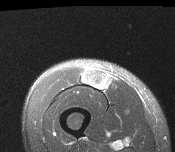
MRI of an extremity soft-tissue mass, one axial slice; position 42 of 116 along the scan axis; T2-weighted fat-saturated; MR volume resampled by the dataset authors to the PET/CT grid (not the native acquisition matrix); 175 × 152 image matrix, field of view 171 × 148 mm. Male patient. From the clinical record (not read from this slice): histological type: pleiomorphic leiomyosarcoma; grade: intermediate; site of the primary tumour: right thigh.
Annotated regions visible in this slice (expert contour drawn on MRI and transferred to this co-registered scan by the dataset authors):
- gross tumour volume including surrounding oedema: box from (x=81, y=70) to (x=109, y=89) px